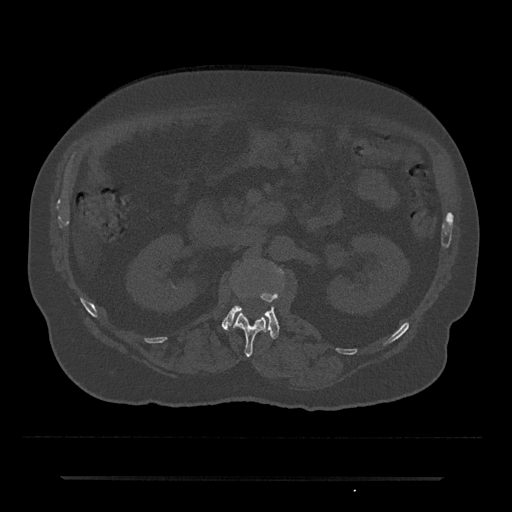
CT including the spine, one axial slice; position 40 of 797 along the scan axis; reconstruction kernel Br40s/3; 120 kVp; bone window (W 1800 / L 400 HU); 0.5 mm slice thickness; 512 × 512 image matrix. Patient: male, 69 years. Case-level facts recorded for this patient, not image findings: primary cancer: prostate.
Outlined on this slice (semi-automatic segmentation, software-assisted and operator-edited):
- L1 vertebra: box from (x=233, y=313) to (x=268, y=357) px
- L2 vertebra: (x=222, y=269)–(x=283, y=339)